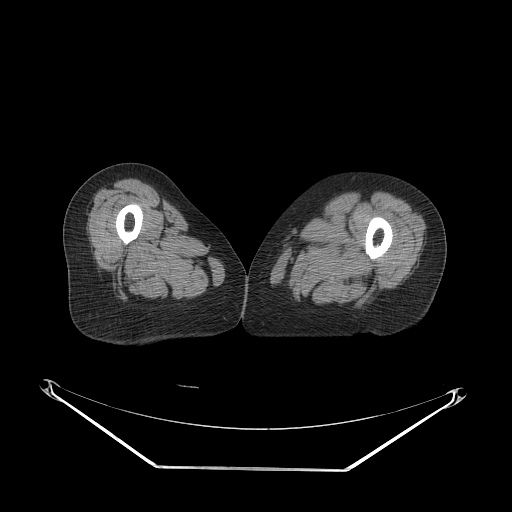
CT of an extremity soft-tissue mass (from a PET/CT study), one axial slice; position 56 of 91 along the scan axis; 140 kVp; soft-tissue window (W 400 / L 40 HU); 3.75 mm slice thickness; 512 × 512 image matrix. Female patient. From the clinical record (not read from this slice): histological type: pleomorphic leiomyosarcoma; grade: high; site of the primary tumour: left thigh.
Outlined on this slice (expert contour drawn on MRI and transferred to this co-registered scan by the dataset authors):
- gross tumour volume including surrounding oedema: bounding box <279,206,302,227> (left, top, right, bottom; pixels)